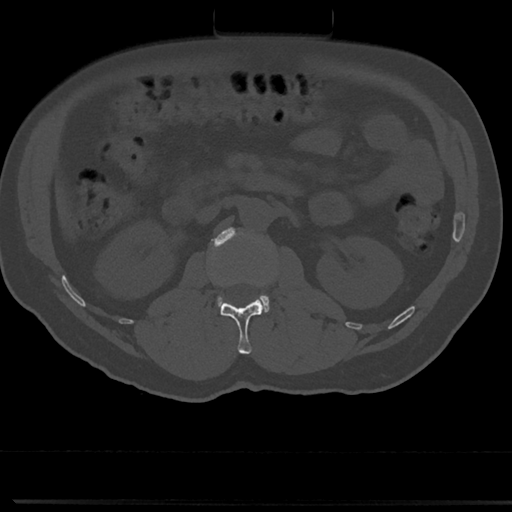
CT including the spine, one axial slice; slice 52 of 817 in the series (ordered by position); reconstruction kernel Br40s/3; 120 kVp; bone window (W 1800 / L 400 HU); 512 × 512 image matrix, field of view 355 × 355 mm. Patient: male, 61 years. From the clinical record (not read from this slice): primary cancer: prostate.
Outlined on this slice (semi-automatically segmented with operator editing):
- L1 vertebra: box from (x=220, y=299) to (x=264, y=355) px
- L2 vertebra: (x=210, y=227)–(x=270, y=313)